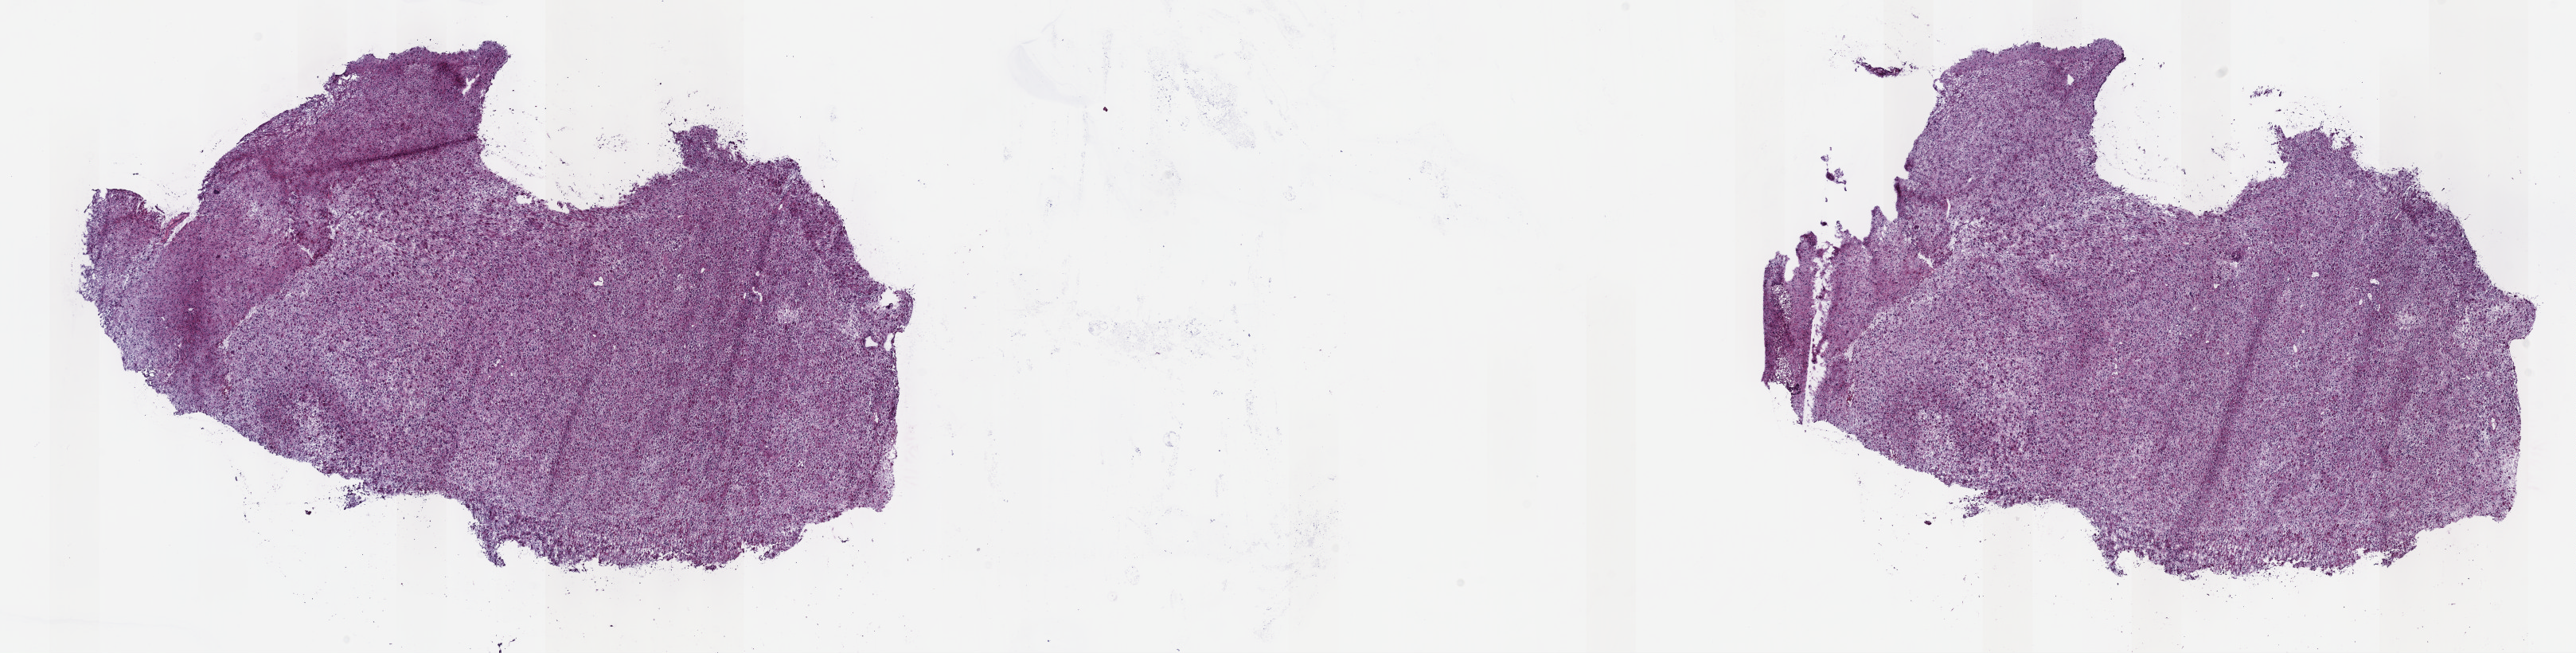
Digitized H&E tissue section (whole slide), shown as a low-resolution overview of the whole scanned area (about 26.2 x 6.6 mm, acquisition: 40x scan); frozen section from the top of the tissue portion; sample: recurrent tumour, brain. Female, age 42 years at initial diagnosis. Composition of this section per pathologist review: tumour cells 80%, tumour nuclei 90%, normal cells 10%, stromal cells 10%, necrosis 0%. Infiltration values recorded for this section: lymphocyte infiltration 0%, monocyte infiltration 0%, neutrophil infiltration 0%.
• this section: recurrent tumour
• patient diagnosis: Oligodendroglioma, NOS (cerebrum)